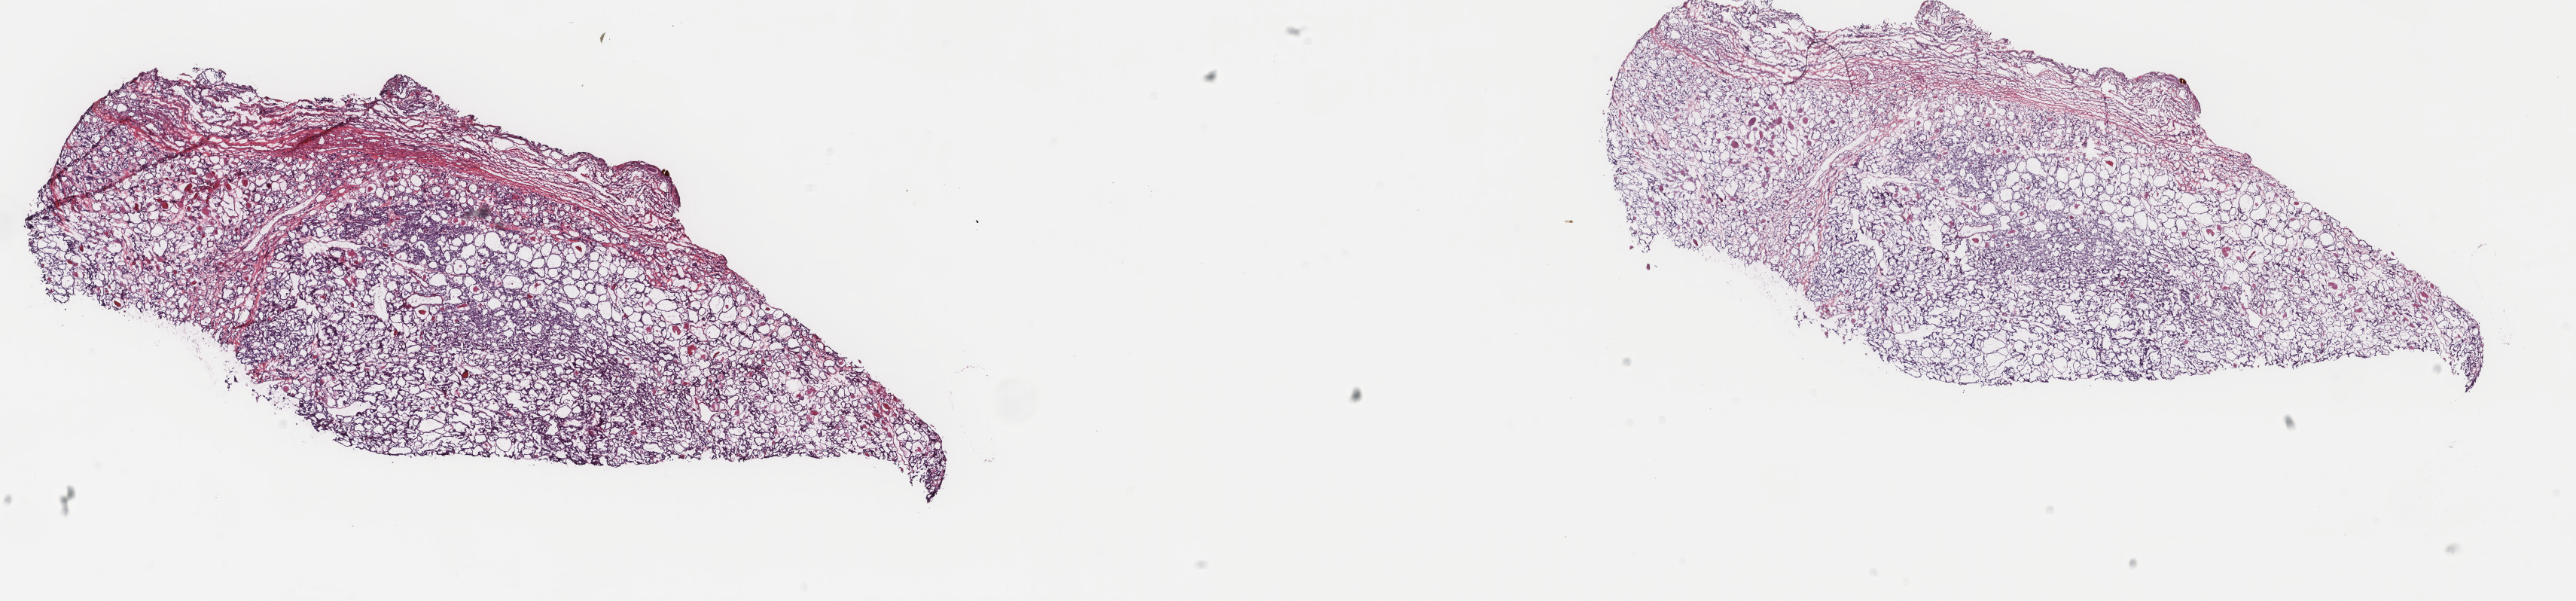
H&E-stained whole-slide image — low-resolution overview of the scanned area, about 27.2 x 6.3 mm. Frozen section. Thyroid, primary tumour sample. Patient: female, age at initial diagnosis 32 years. Composition of this section per pathologist review: tumour cells 85%, tumour nuclei 95%, normal cells 0%, stromal cells 15%, necrosis 0%. Infiltration values recorded for this section: lymphocyte infiltration 0%, monocyte infiltration 0%, neutrophil infiltration 0%.
- TNM: T2 N0 MX
- histologic diagnosis: Papillary carcinoma, follicular variant (thyroid gland)
- AJCC pathologic stage: I